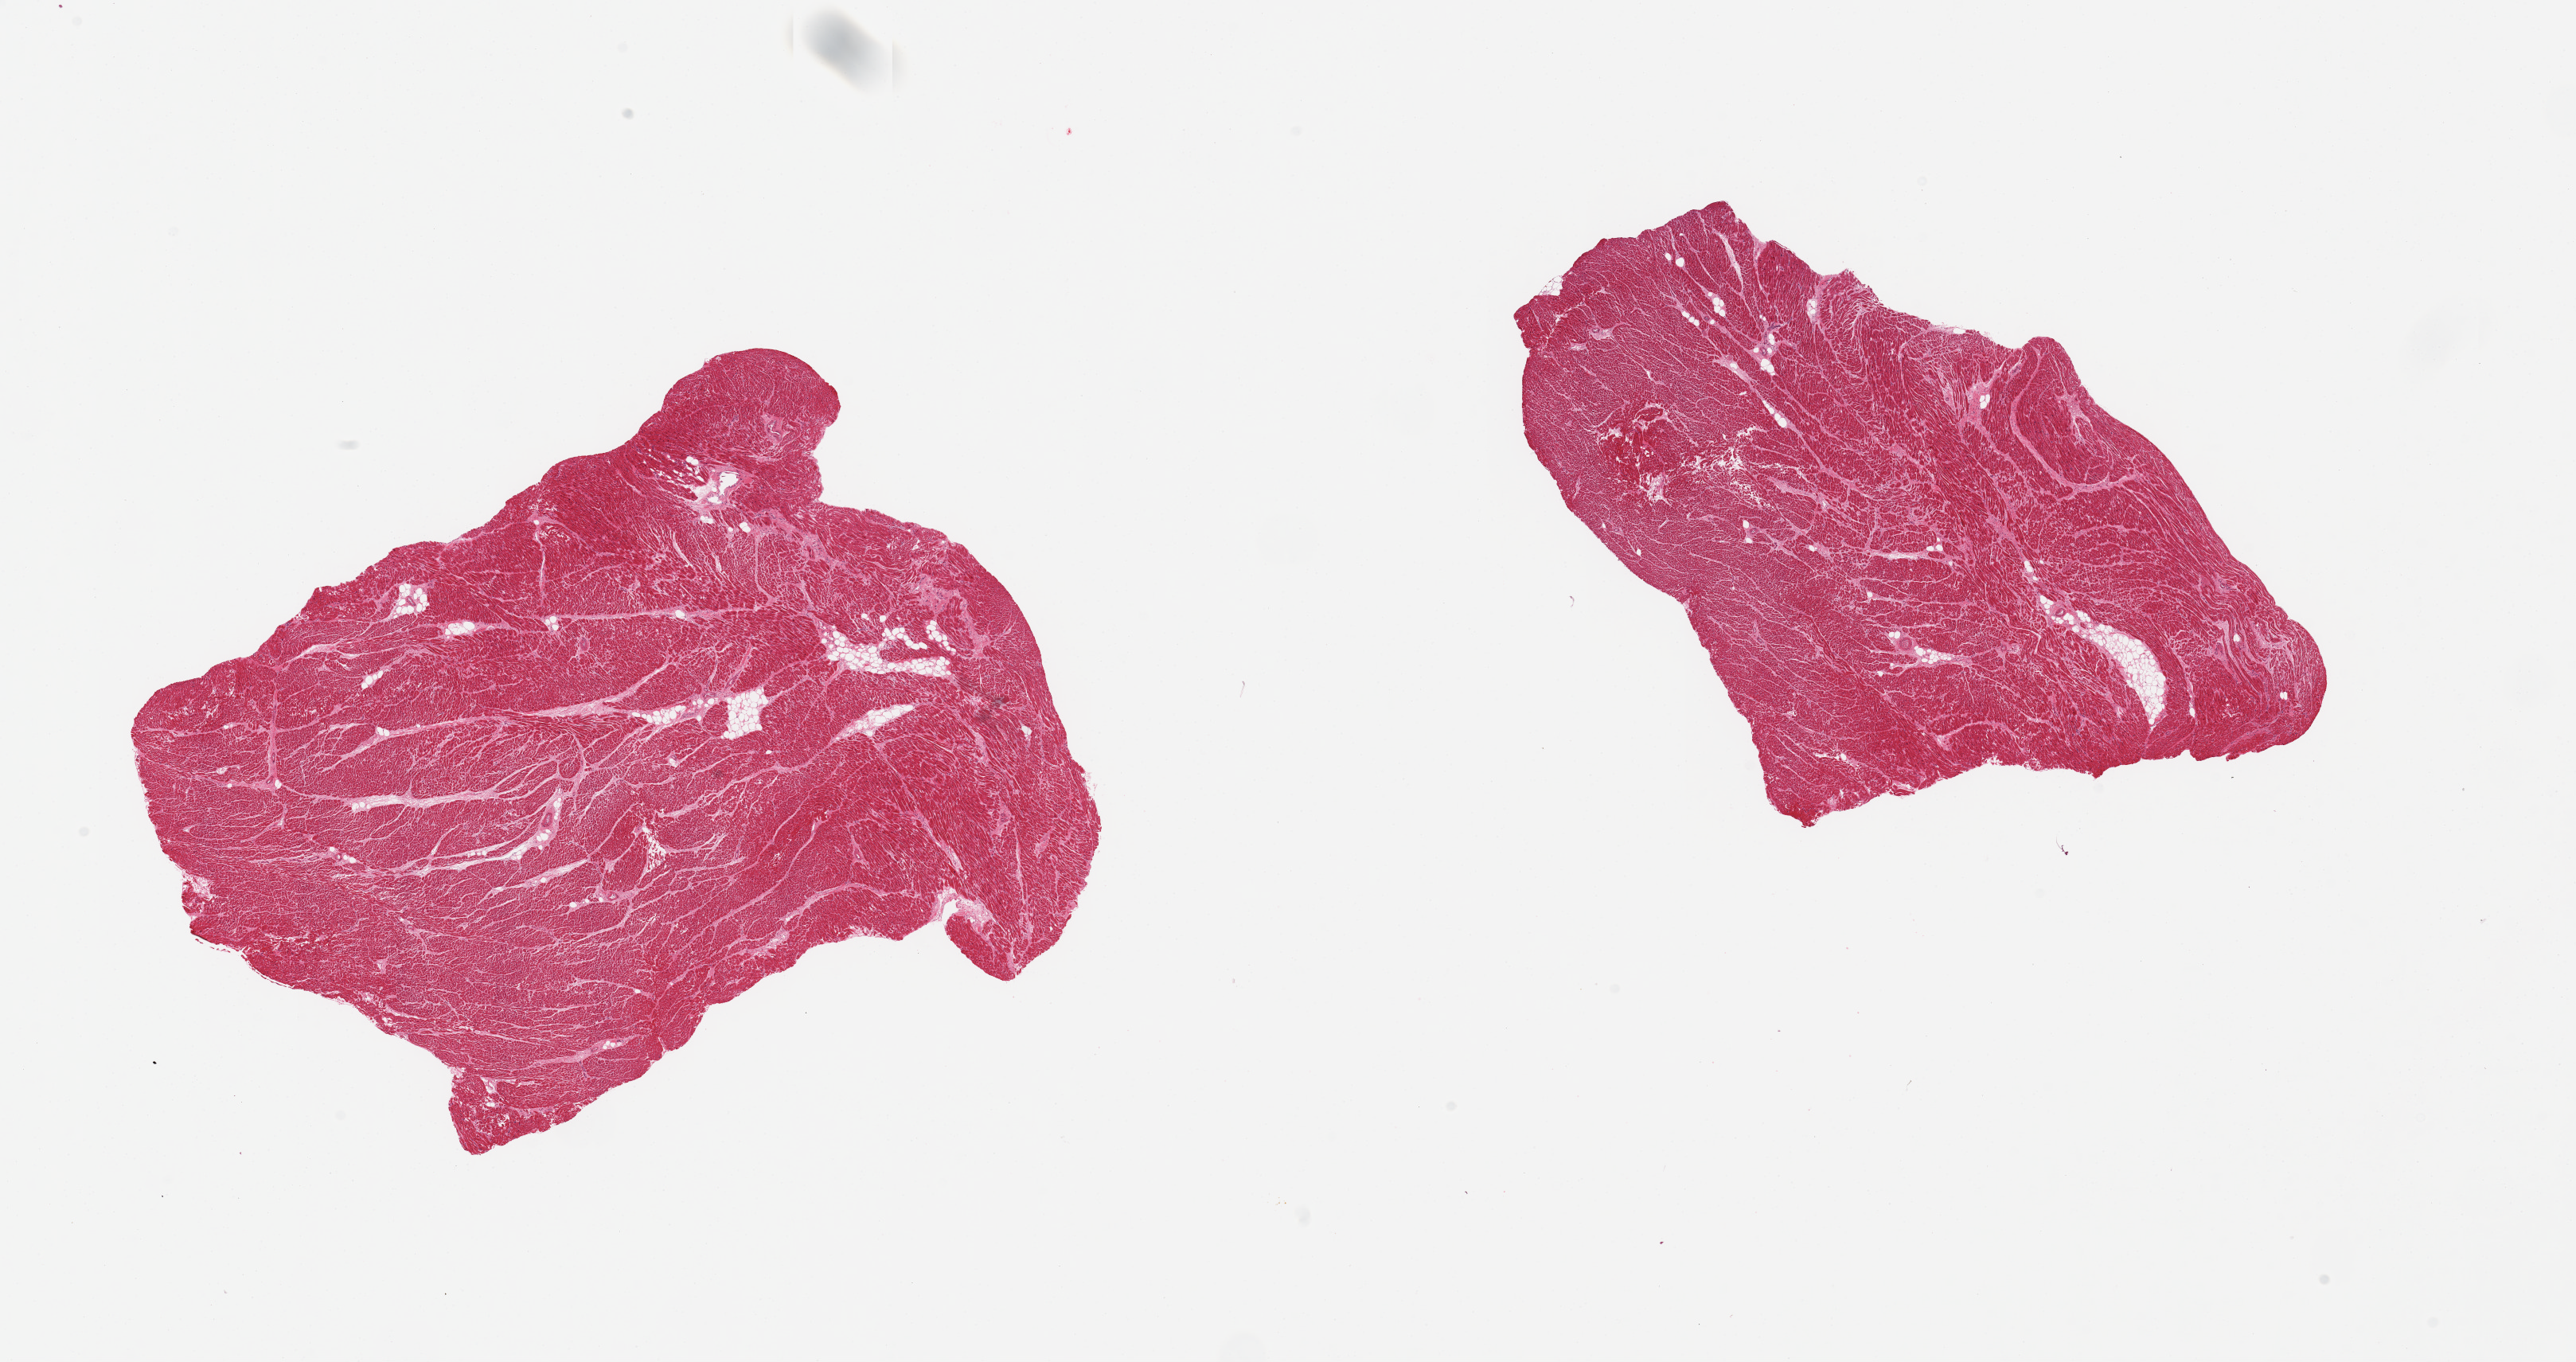
H&E whole-slide image, a low-resolution overview of the entire scanned area, about 25.6 x 13.5 mm (from a 20x scan), PAXgene-fixed, paraffin-embedded tissue, section of heart (target tissue), tissue donor sample. Donor: male.
* reviewer comment on this tissue sample: 2 pieces; 5% internal fat